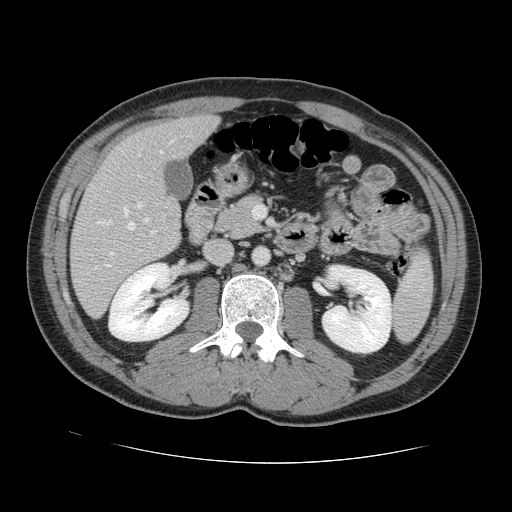
Contrast-enhanced abdominal CT, one axial slice. Slice 58 of 131 in the series (ordered by position). Intravenous contrast given. Soft-tissue window (W 400 / L 40 HU). 2.5 mm slice thickness. 512 × 512 image matrix, field of view 380 × 380 mm. Male patient, age 40 years. Case-level facts recorded for this patient, not image findings: diagnosis: colorectal cancer liver metastases, imaged before liver resection.
Outlined on this slice (expert manual segmentation):
- hepatic veins: bounding box <98,140,174,256> (left, top, right, bottom; pixels)
- liver: <72,116,216,315>
- planned liver remnant (the part of the liver to remain after resection): <113,117,217,175>
- portal vein (with intrahepatic branches): <105,154,156,267>